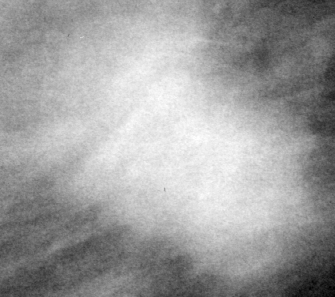
Cropped region of a digitized screen-film mammogram centred on a radiologist-marked abnormality; right breast; MLO view.
- Mass, shape irregular / architectural distortion, margins obscured / spiculated; BI-RADS assessment category 5; pathology result (as recorded, not read from the image): malignant.